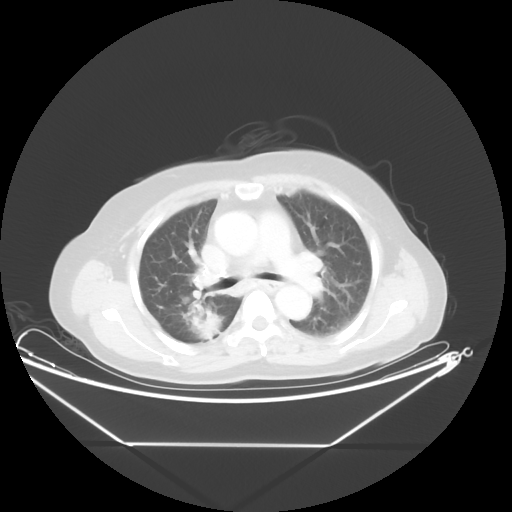
Chest CT, one axial slice; slice 30 of 48 in the series (ordered by position); reconstruction kernel STANDARD; lung window (W 1500 / L -600 HU); 5 mm slice thickness; 512 × 512 image matrix, field of view 462 × 462 mm. Female patient, age 62 years. Case-level facts recorded for this patient, not image findings: clinical TNM (as recorded): T1c N0 M0; histopathological grade: G2-3.
Annotated regions visible in this slice (bounding box drawn by a radiologist):
- lung tumour (recorded histology: adenocarcinoma): bounding box (x1, y1, x2, y2) in pixels: (185, 296, 231, 348)